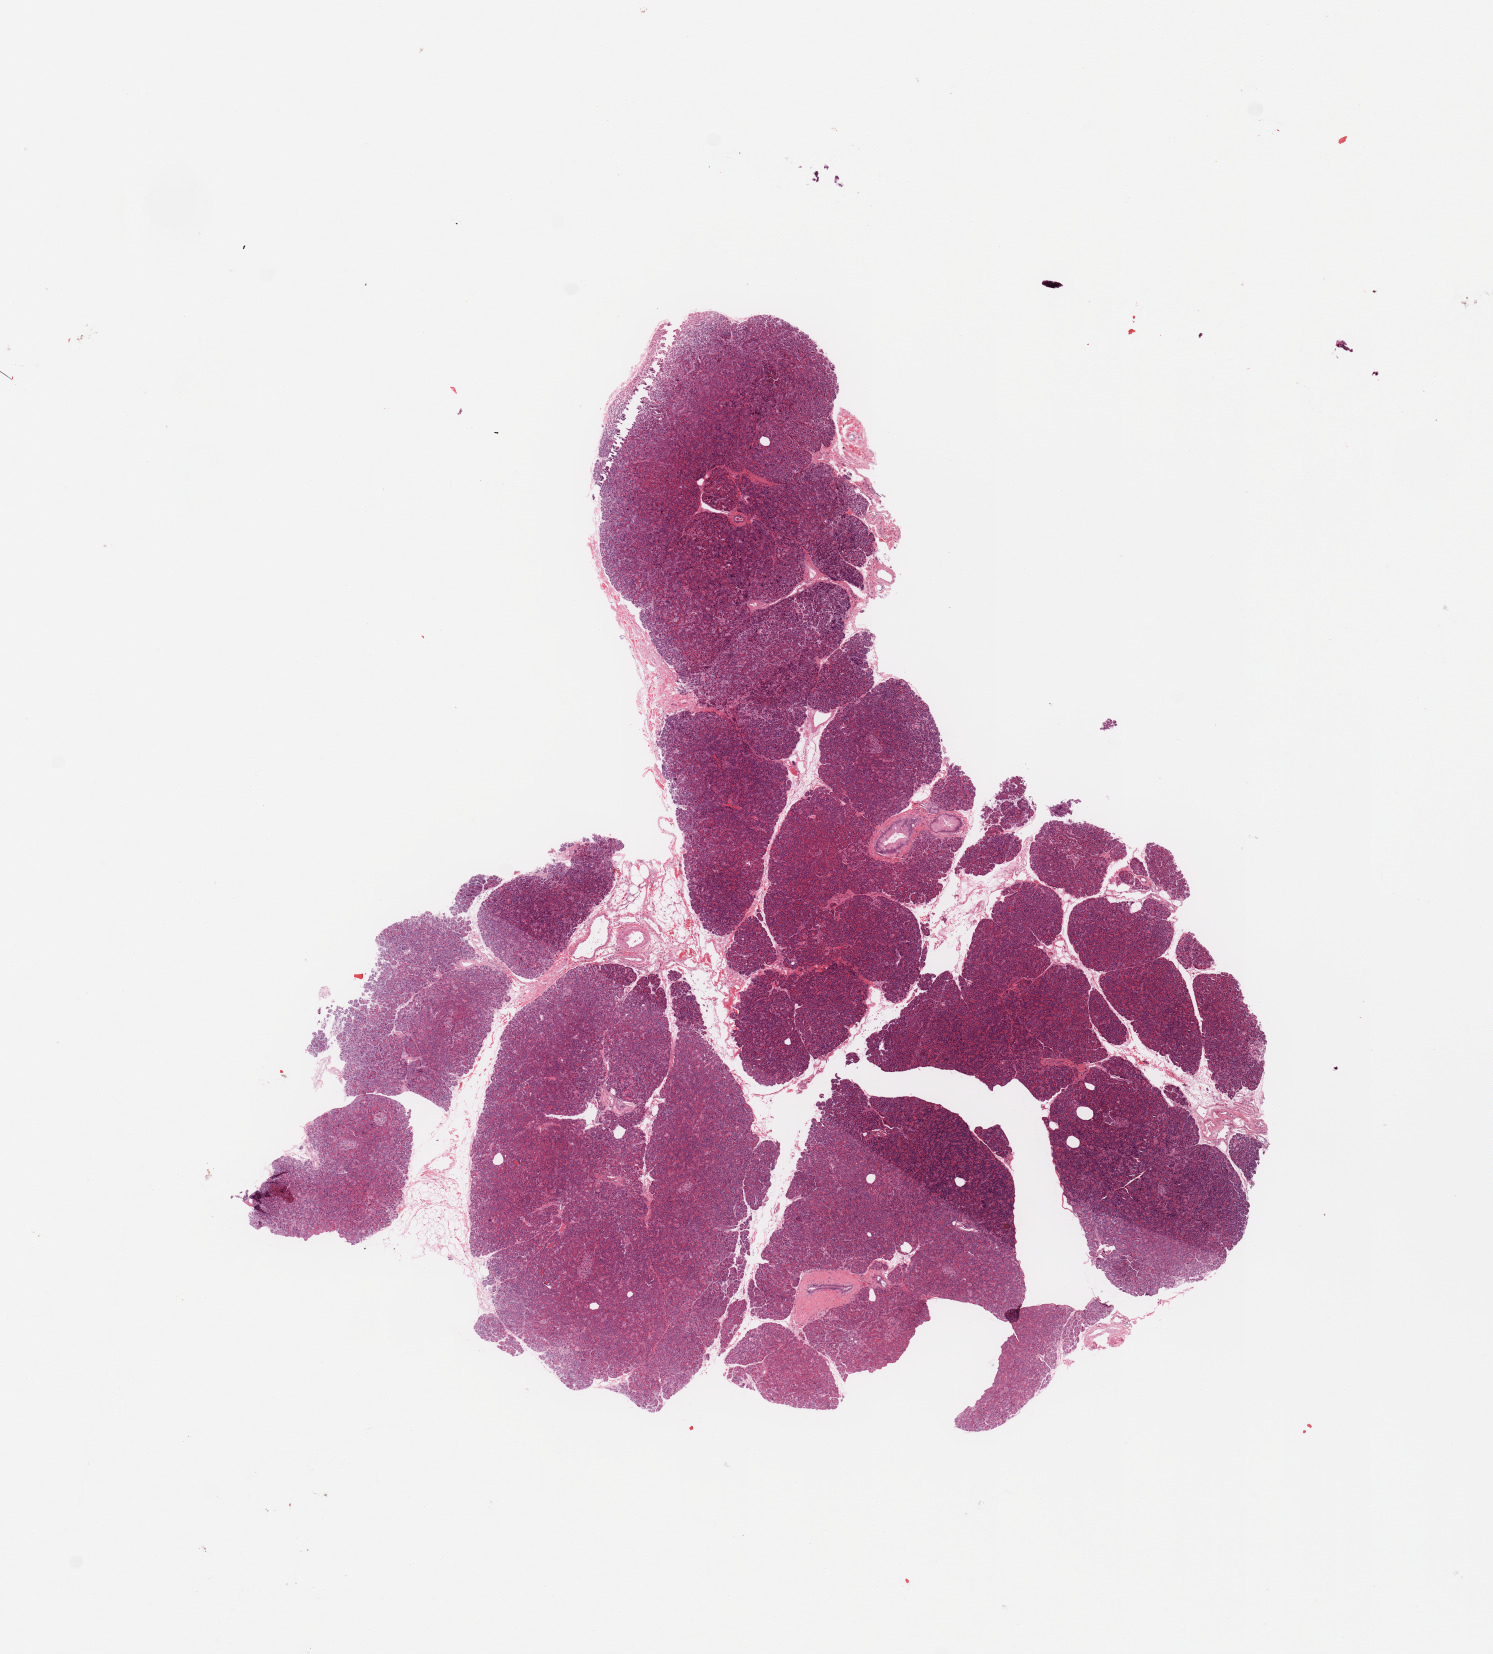
Digitized H&E tissue section (whole slide), whole scanned area (about 11.8 x 13.1 mm, from a 20x scan) shown as a low-resolution overview. Normal (non-tumour) tissue sample, sampled site: pancreas. 59-year-old female patient.
• this section: normal (non-tumour) tissue from the same patient
• patient diagnosis: Infiltrating duct carcinoma, NOS